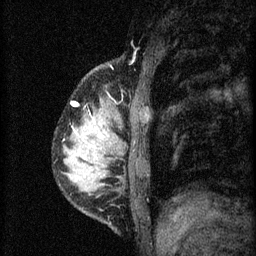
Breast MRI (dynamic contrast-enhanced), one sagittal slice. Position 12 of 60 along the scan axis. 3 images stored at this slice position (order not interpretable as contrast timing). 1.5 T. TE 4.2 ms, TR 8.2 ms. 2 mm slice thickness. 256 × 256 image matrix, field of view 180 × 180 mm. Female patient, age 37 years.
Outlined on this slice (semi-automatically segmented with operator editing):
- analysis volume of interest (the breast-tissue region the enhancement analysis was run in; not a lesion): bounding box (x1, y1, x2, y2) in pixels: (62, 96, 140, 181)
- tumour enhancement mask (voxels above the 70 % enhancement threshold inside the analysis volume of interest): (71, 102, 95, 131)